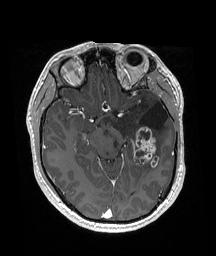
Brain MRI from a brain-tumour surgery series, one axial slice; position 105 of 192 along the scan axis; T1-weighted post-contrast; 1 mm slice thickness; 216 × 256 image matrix, field of view 211 × 250 mm. From the clinical record (not read from this slice): histopathology: Glioneuronal tumor; WHO grade: 2.
Outlined on this slice (expert manual segmentation):
- previous resection cavity: bounding box [x1, y1, x2, y2] px = [140, 103, 168, 130]
- tumour: [132, 126, 159, 167]